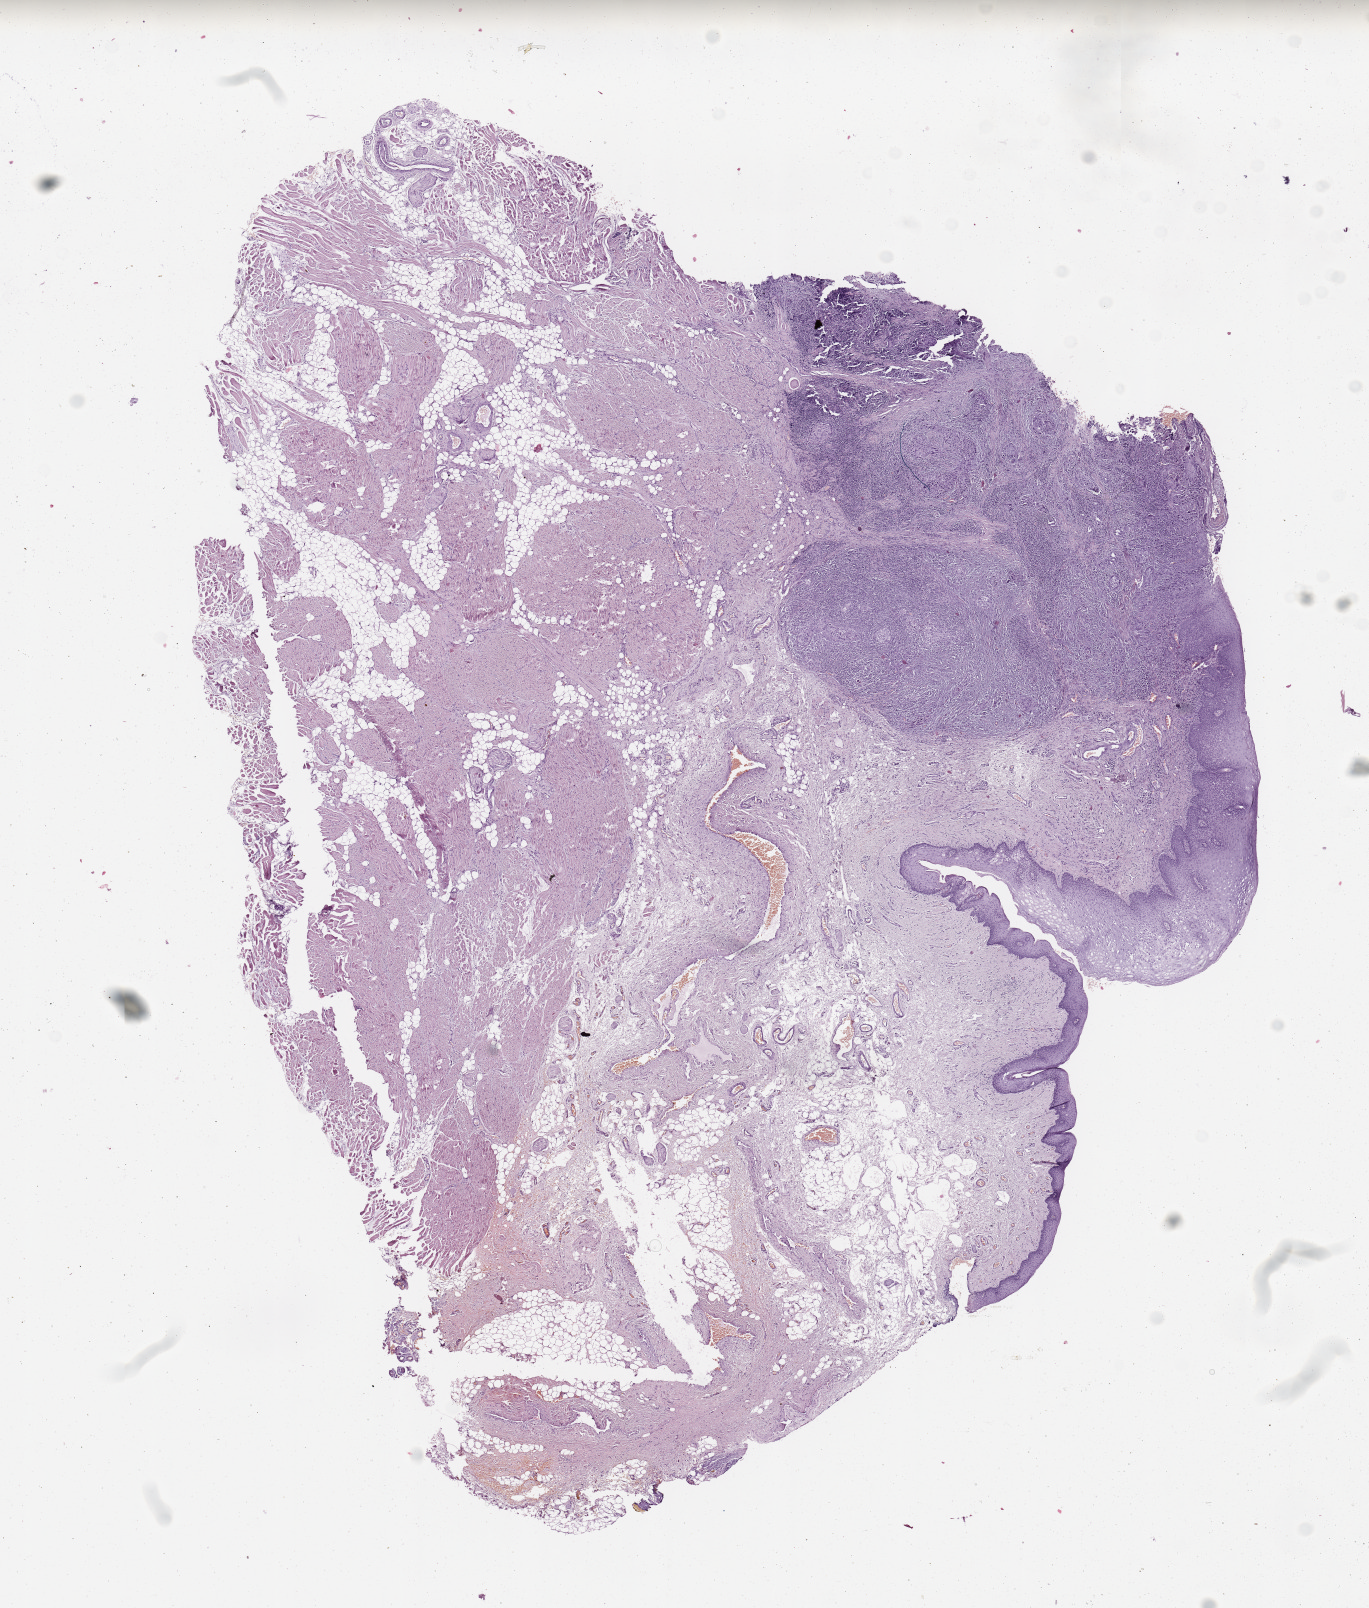
Hematoxylin and eosin (H&E) stained whole-slide image — whole scanned area (about 10.8 x 12.7 mm, acquisition: 20x scan) shown as a low-resolution overview; head and neck, tissue type not recorded. Male, 61 y/o.
Patient diagnosis: Squamous cell carcinoma, NOS.